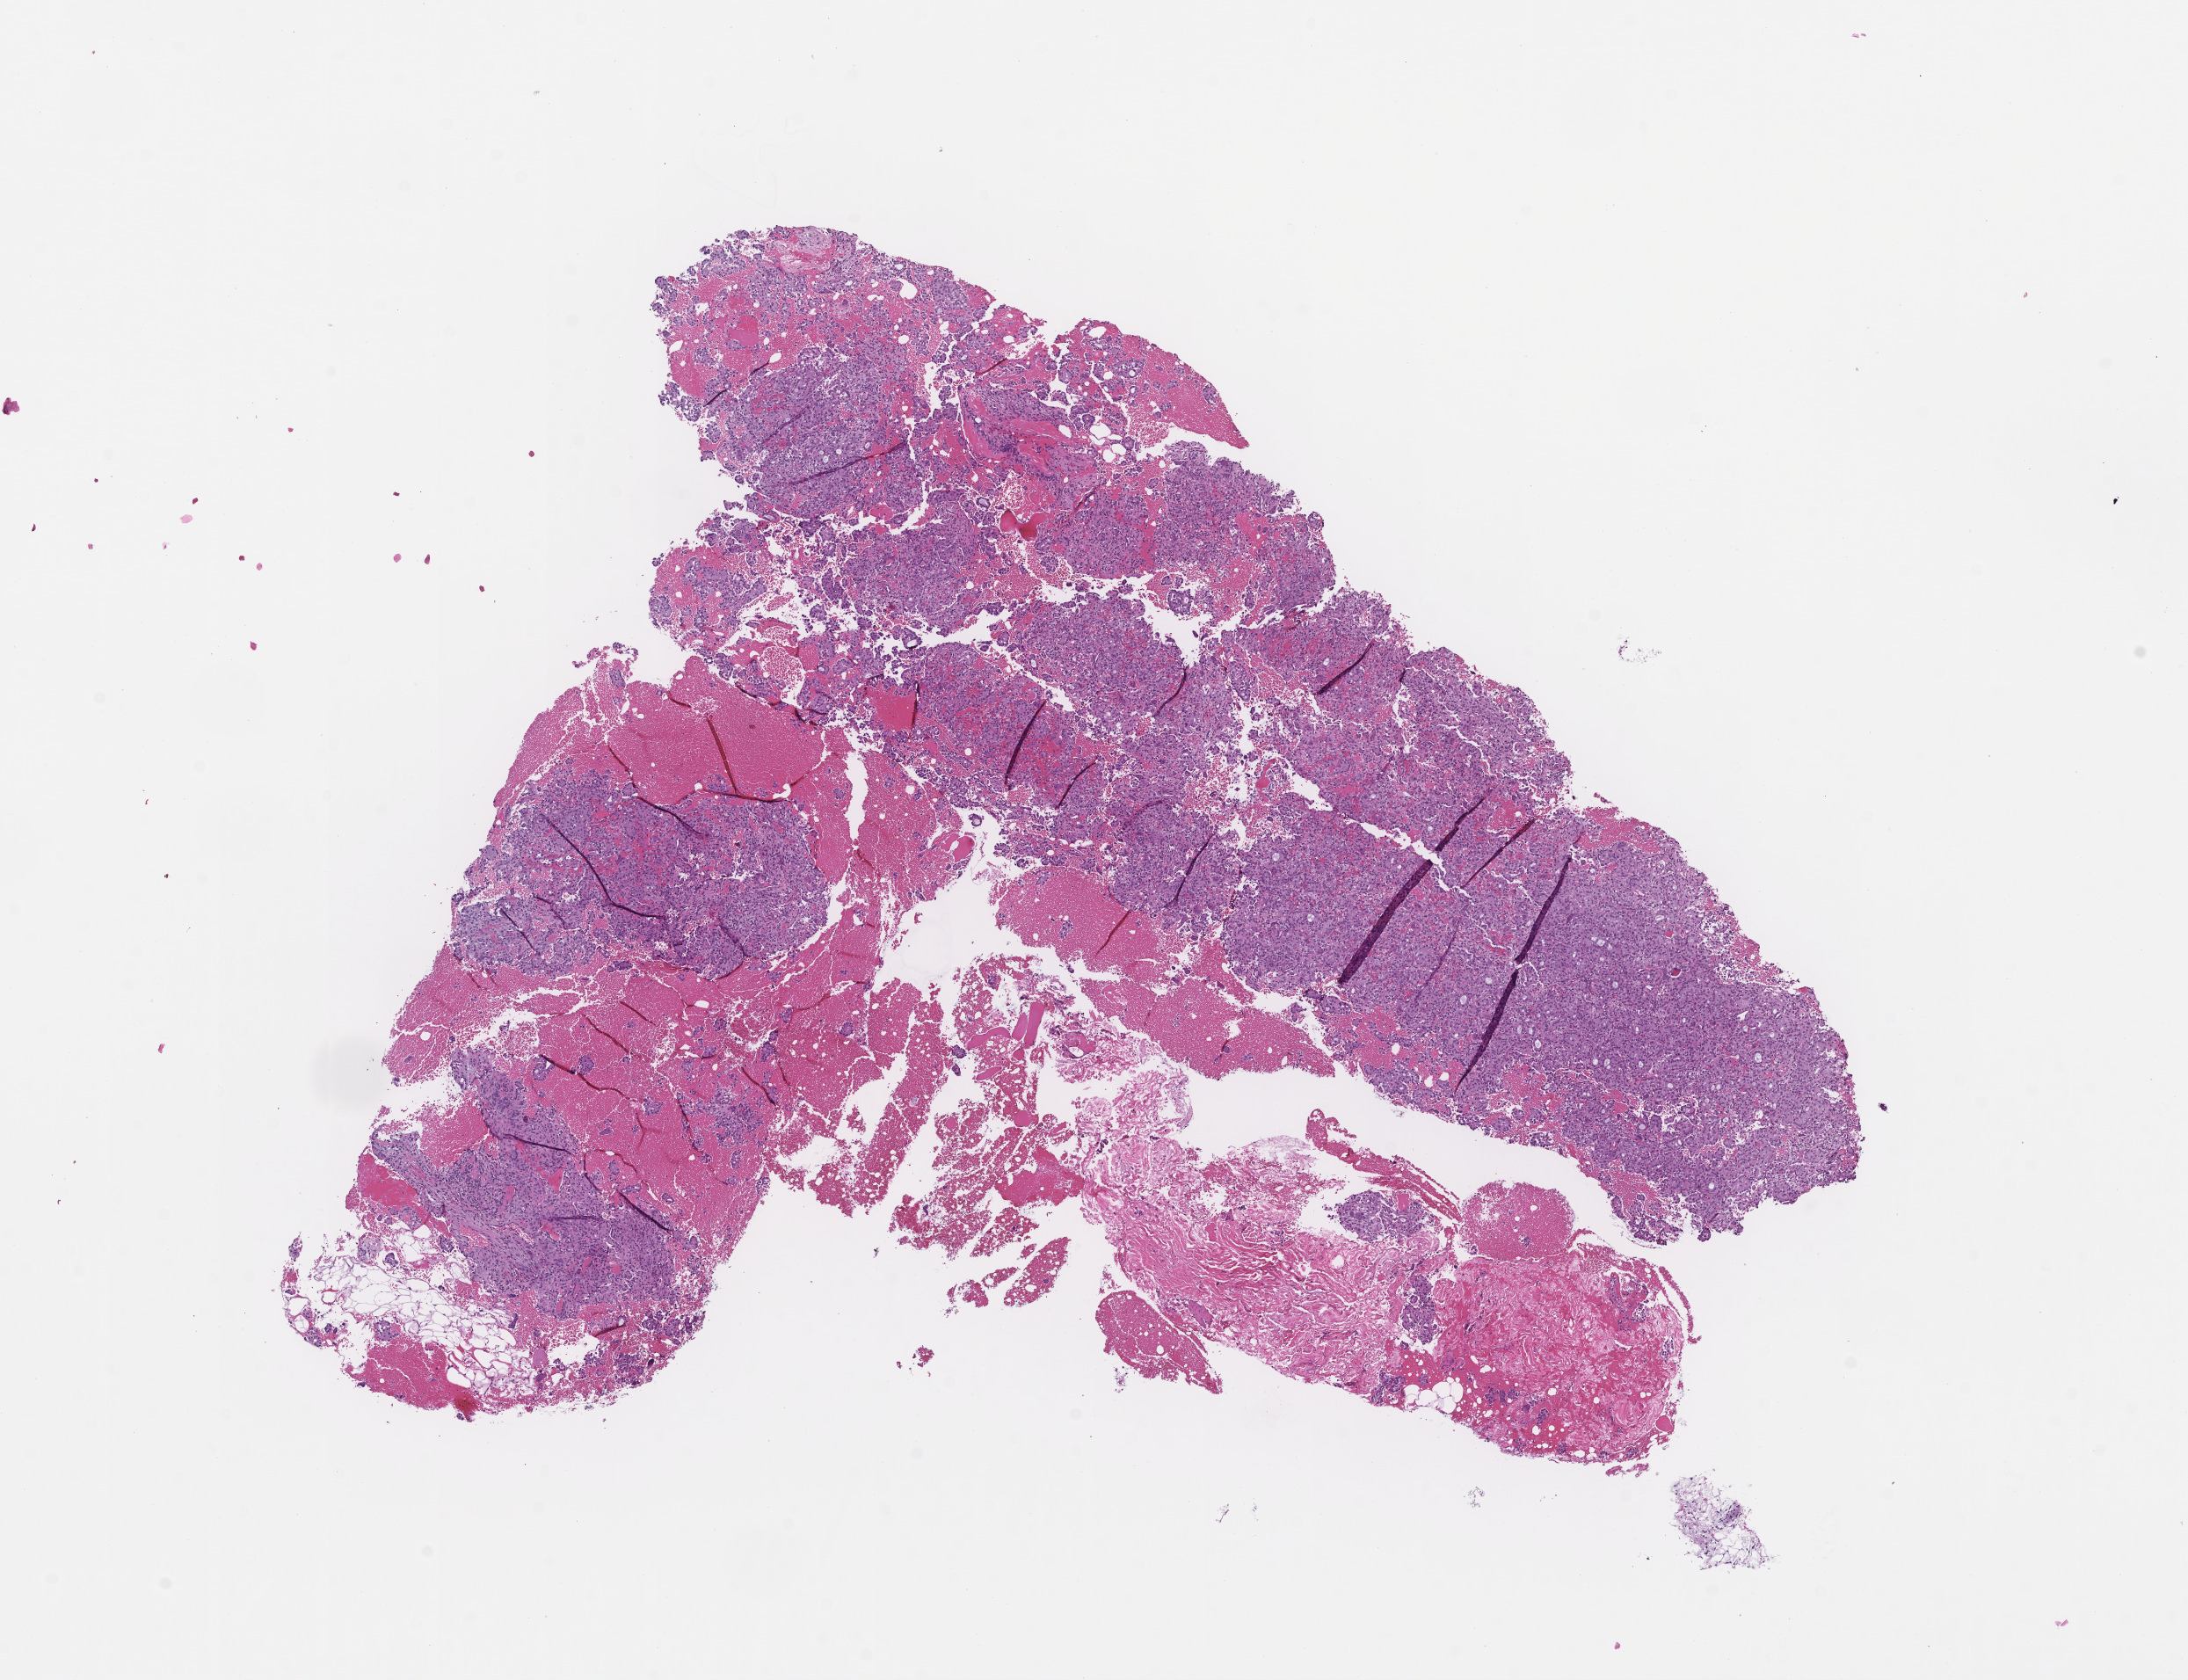
Digitized hematoxylin and eosin (H&E)-stained section — a low-resolution overview of the entire scanned area, about 10.1 x 7.7 mm; formalin-fixed, paraffin-embedded (FFPE) tissue. Female patient.
This section: metastatic tumor tissue. Primary diagnosis of the patient: Invasive Breast Carcinoma.